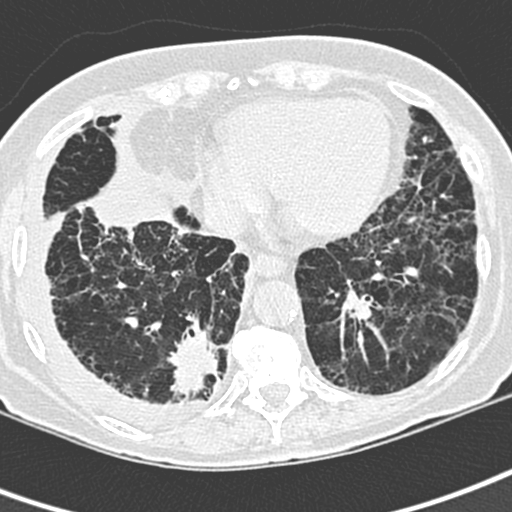
Low-dose screening chest CT, one axial slice. Slice 85 of 220 in the series (ordered by position). Lung window (W 1500 / L -600 HU). 1.3 mm slice thickness. 512 × 512 image matrix.
Outlined on this slice (expert manual segmentation):
- lesion 1 (tumor, lower lobe of right lung): bounding box <169,316,220,398> (left, top, right, bottom; pixels)